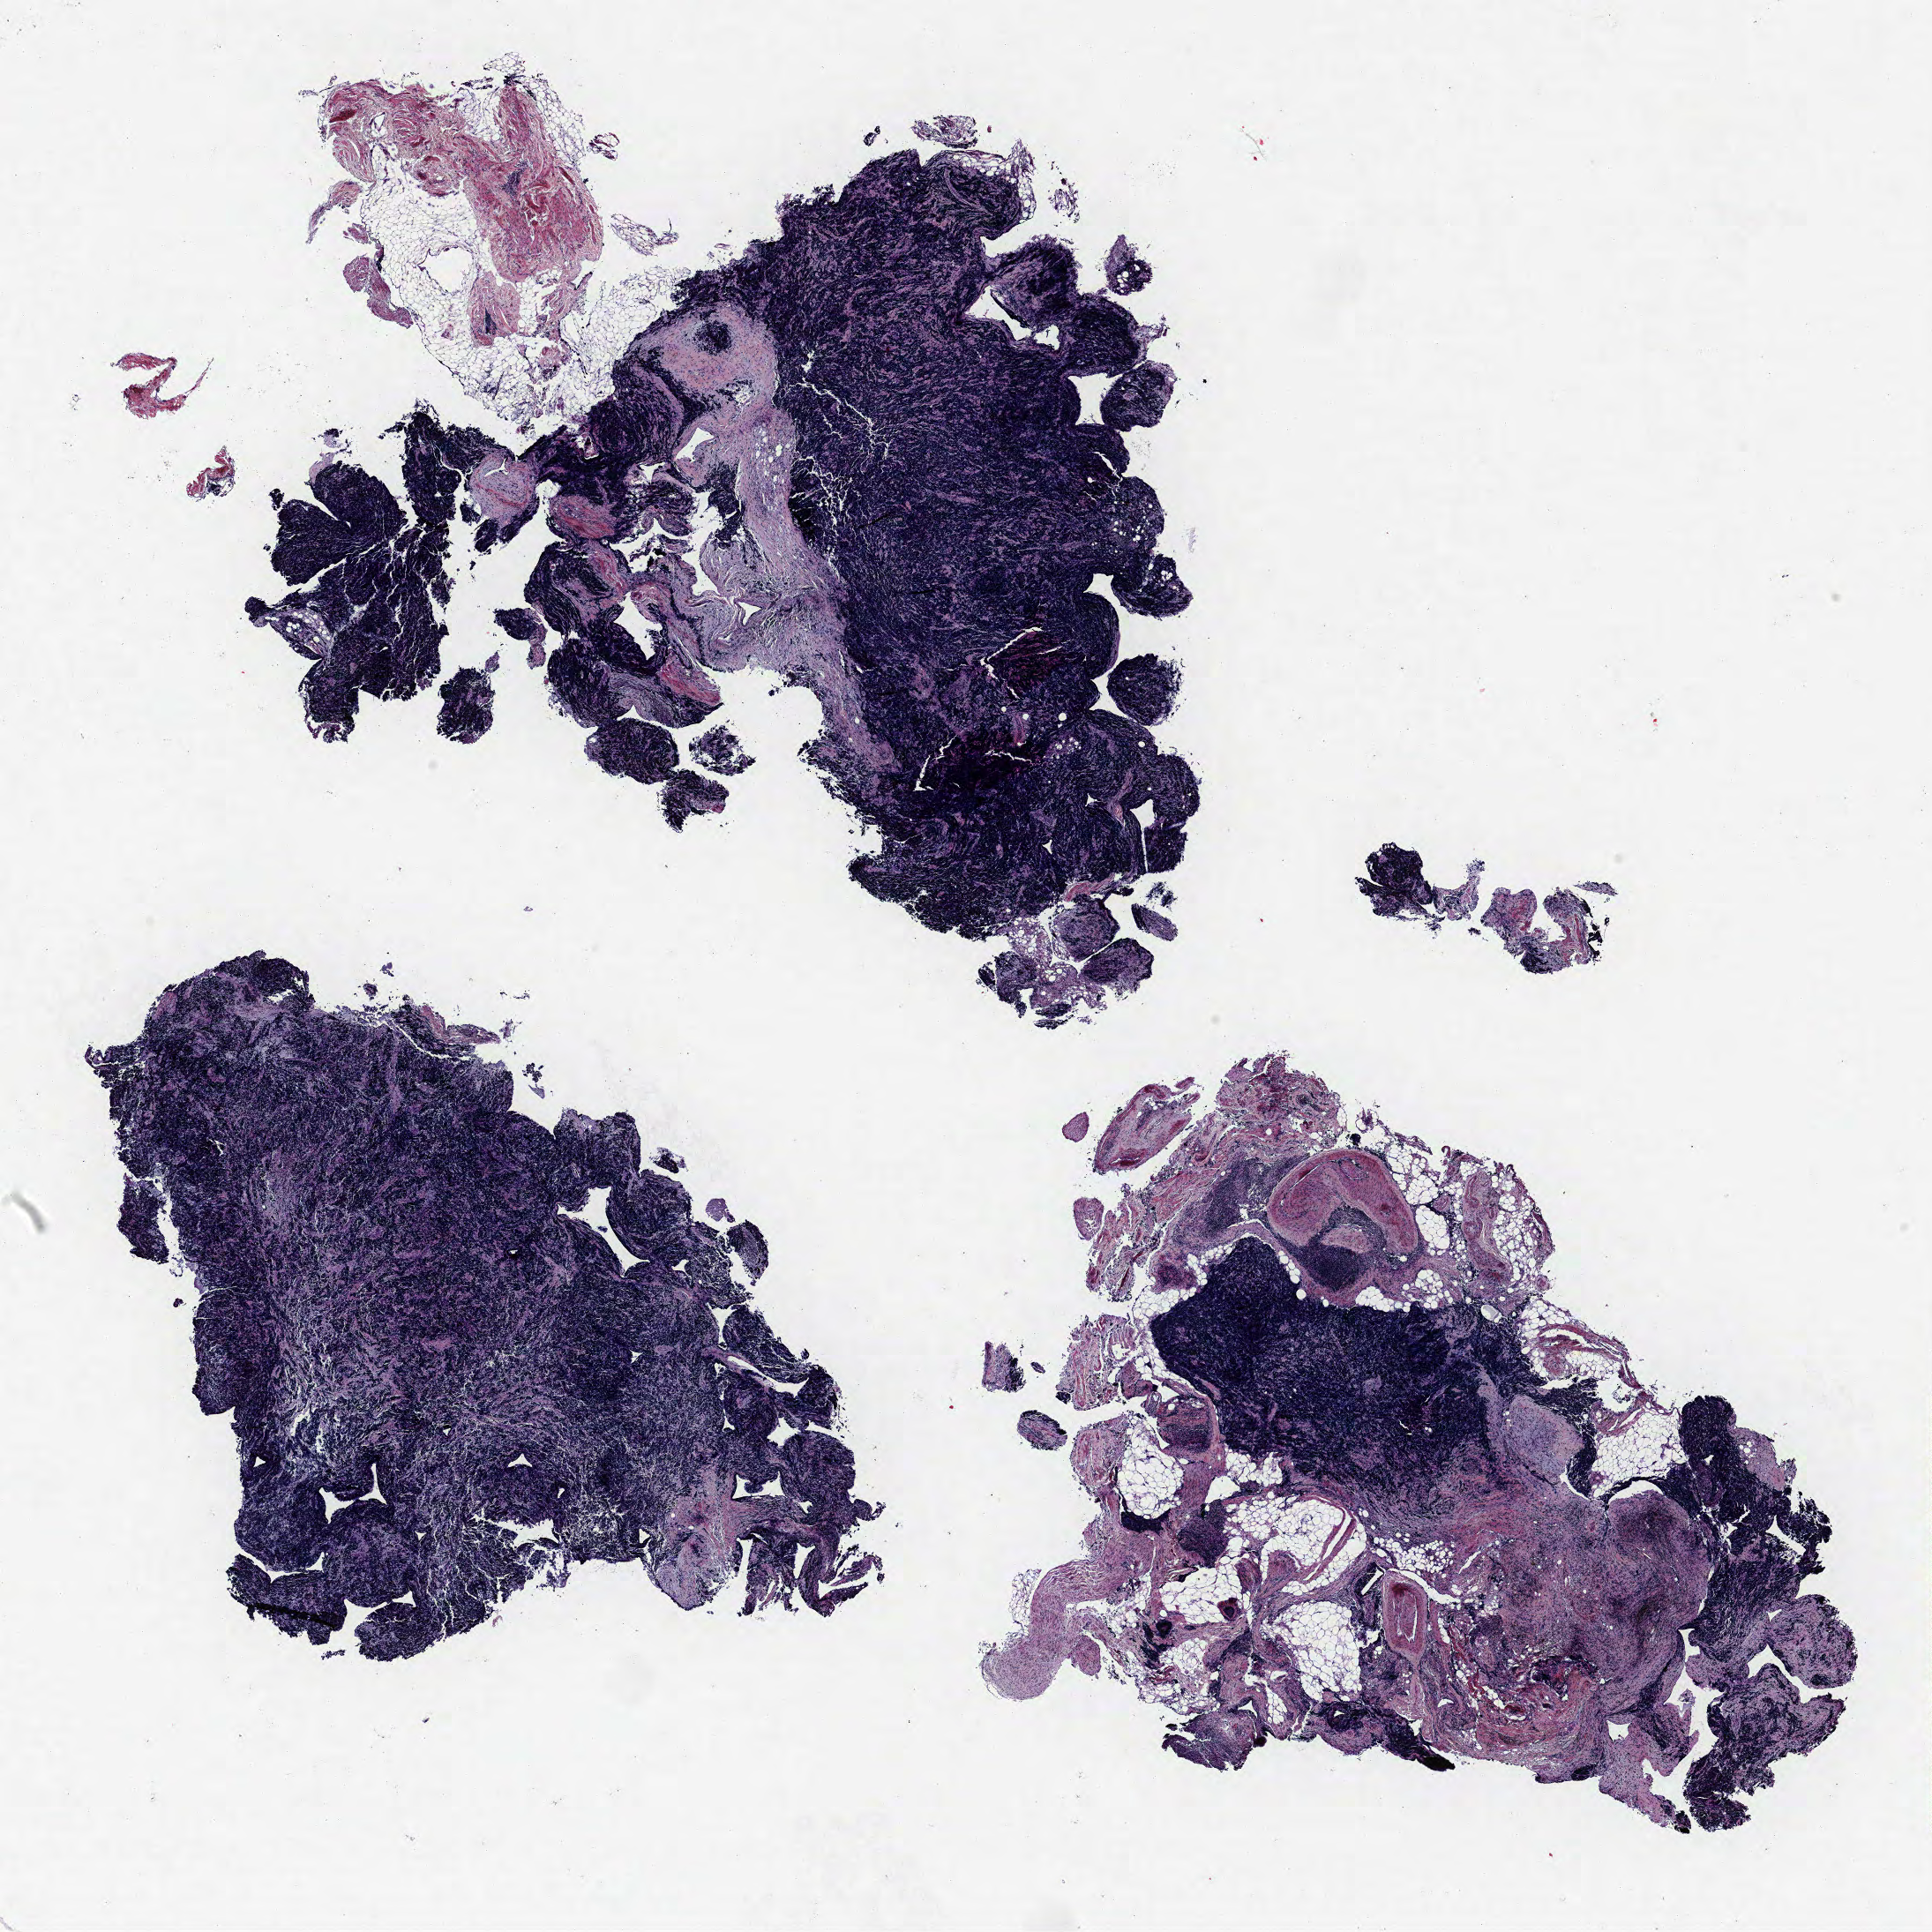
Whole-slide histology image, Hematoxylin and eosin (H&E) stained, a low-resolution overview of the entire scanned area, about 17.5 x 17.5 mm (from a 40x scan), FFPE section, lung. Female patient, aged 65 at enrolment. Grade: cannot be assessed (GX).
Participant's lung-cancer diagnosis: Small cell carcinoma, NOS. Tumour size (pathology): 10 mm. Stage (AJCC 6th edition): IIIA. Primary tumour location (clinical record): right upper lobe.